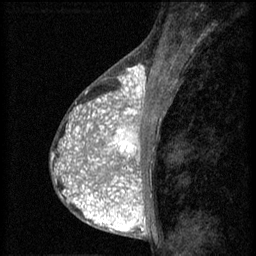
Breast MRI (dynamic contrast-enhanced), one sagittal slice; position 28 of 60 along the scan axis; 3 images stored at this slice position (order not interpretable as contrast timing); 1.5 T; TE 4.2 ms, TR 8.2 ms; 2 mm slice thickness; 256 × 256 image matrix, field of view 180 × 180 mm. Patient: female, 38 years.
Structures marked on this image (semi-automatically segmented with operator editing):
- analysis volume of interest (the breast-tissue region the enhancement analysis was run in; not a lesion): bounding box <92,112,152,171> (left, top, right, bottom; pixels)
- tumour enhancement mask (voxels above the 70 % enhancement threshold inside the analysis volume of interest): <92,112,142,171>